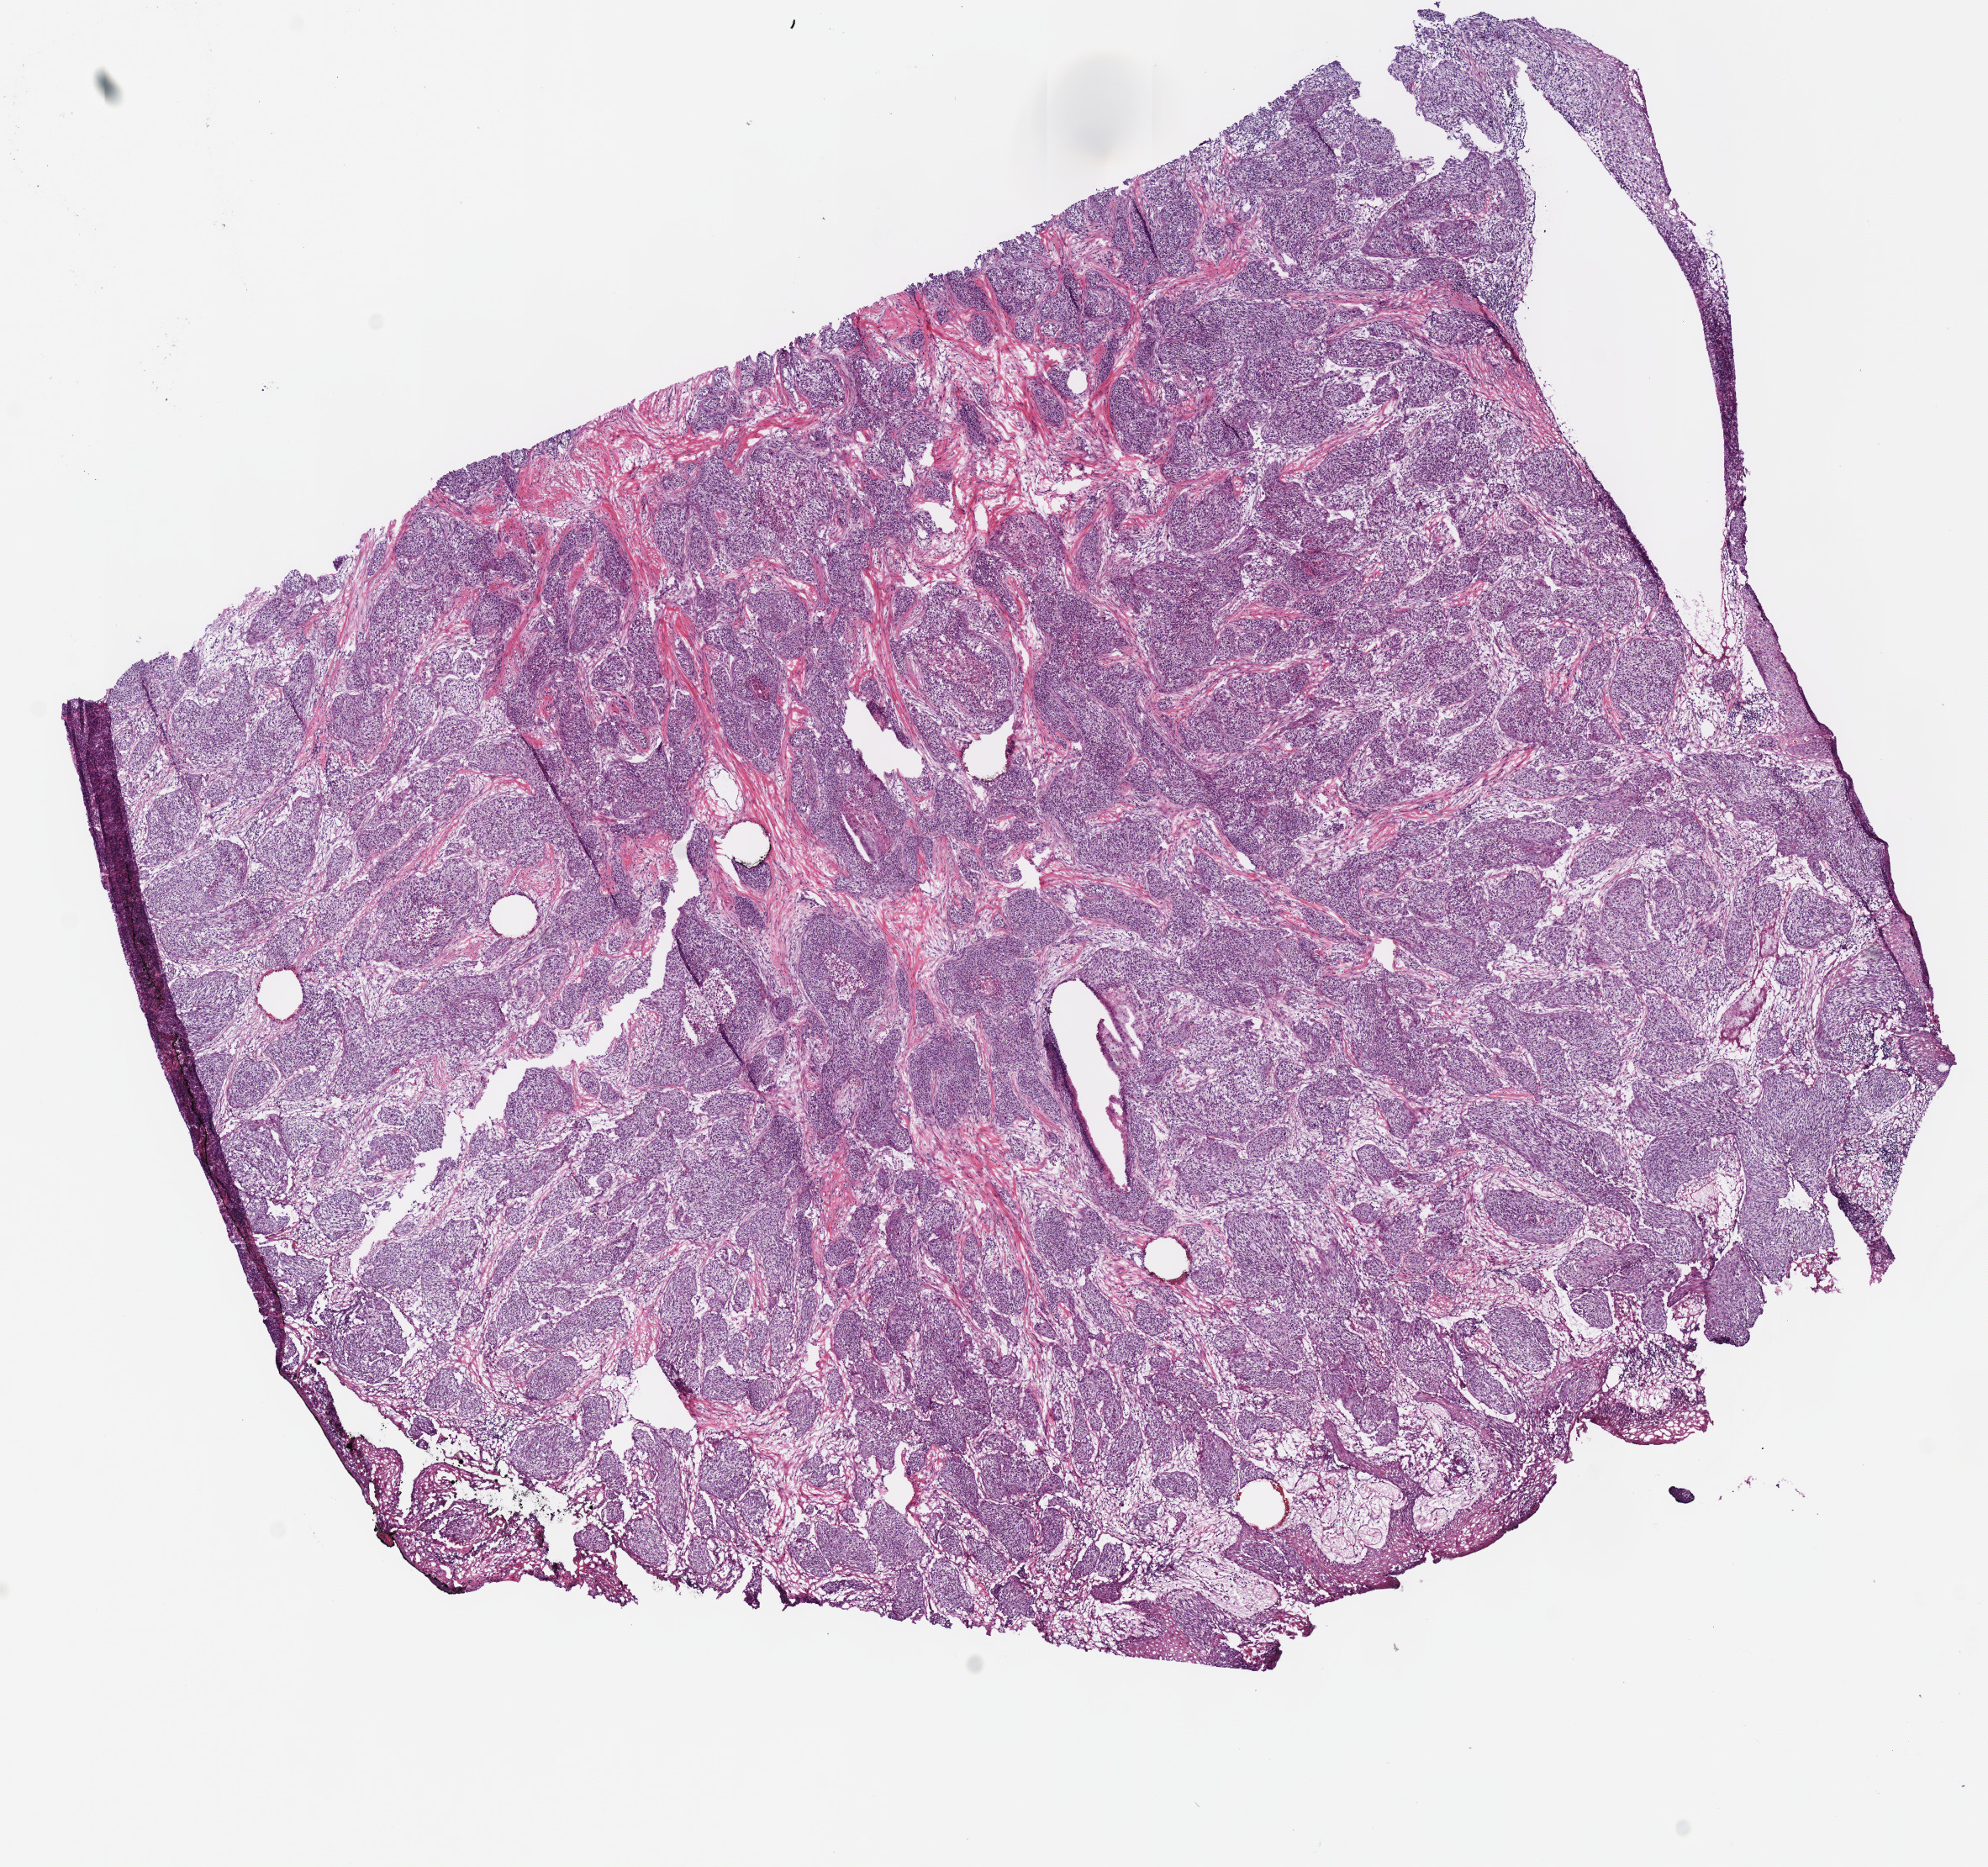
Whole-slide histology image, H&E-stained — shown as a low-resolution overview of the whole scanned area (about 9.3 x 8.7 mm); frozen section from the bottom of the tissue portion; primary tumour sample from the head and neck. Male patient; age at initial diagnosis 69 years. Histologic grade: G1 (well differentiated). Pathologist review of this section (percent, as recorded): tumour cells 88%, tumour nuclei 70%, normal cells 0%, stromal cells 10%, necrosis 2%.
AJCC pathologic stage: IVA (7th edition). Diagnosis: Squamous cell carcinoma, NOS (oropharynx, NOS).